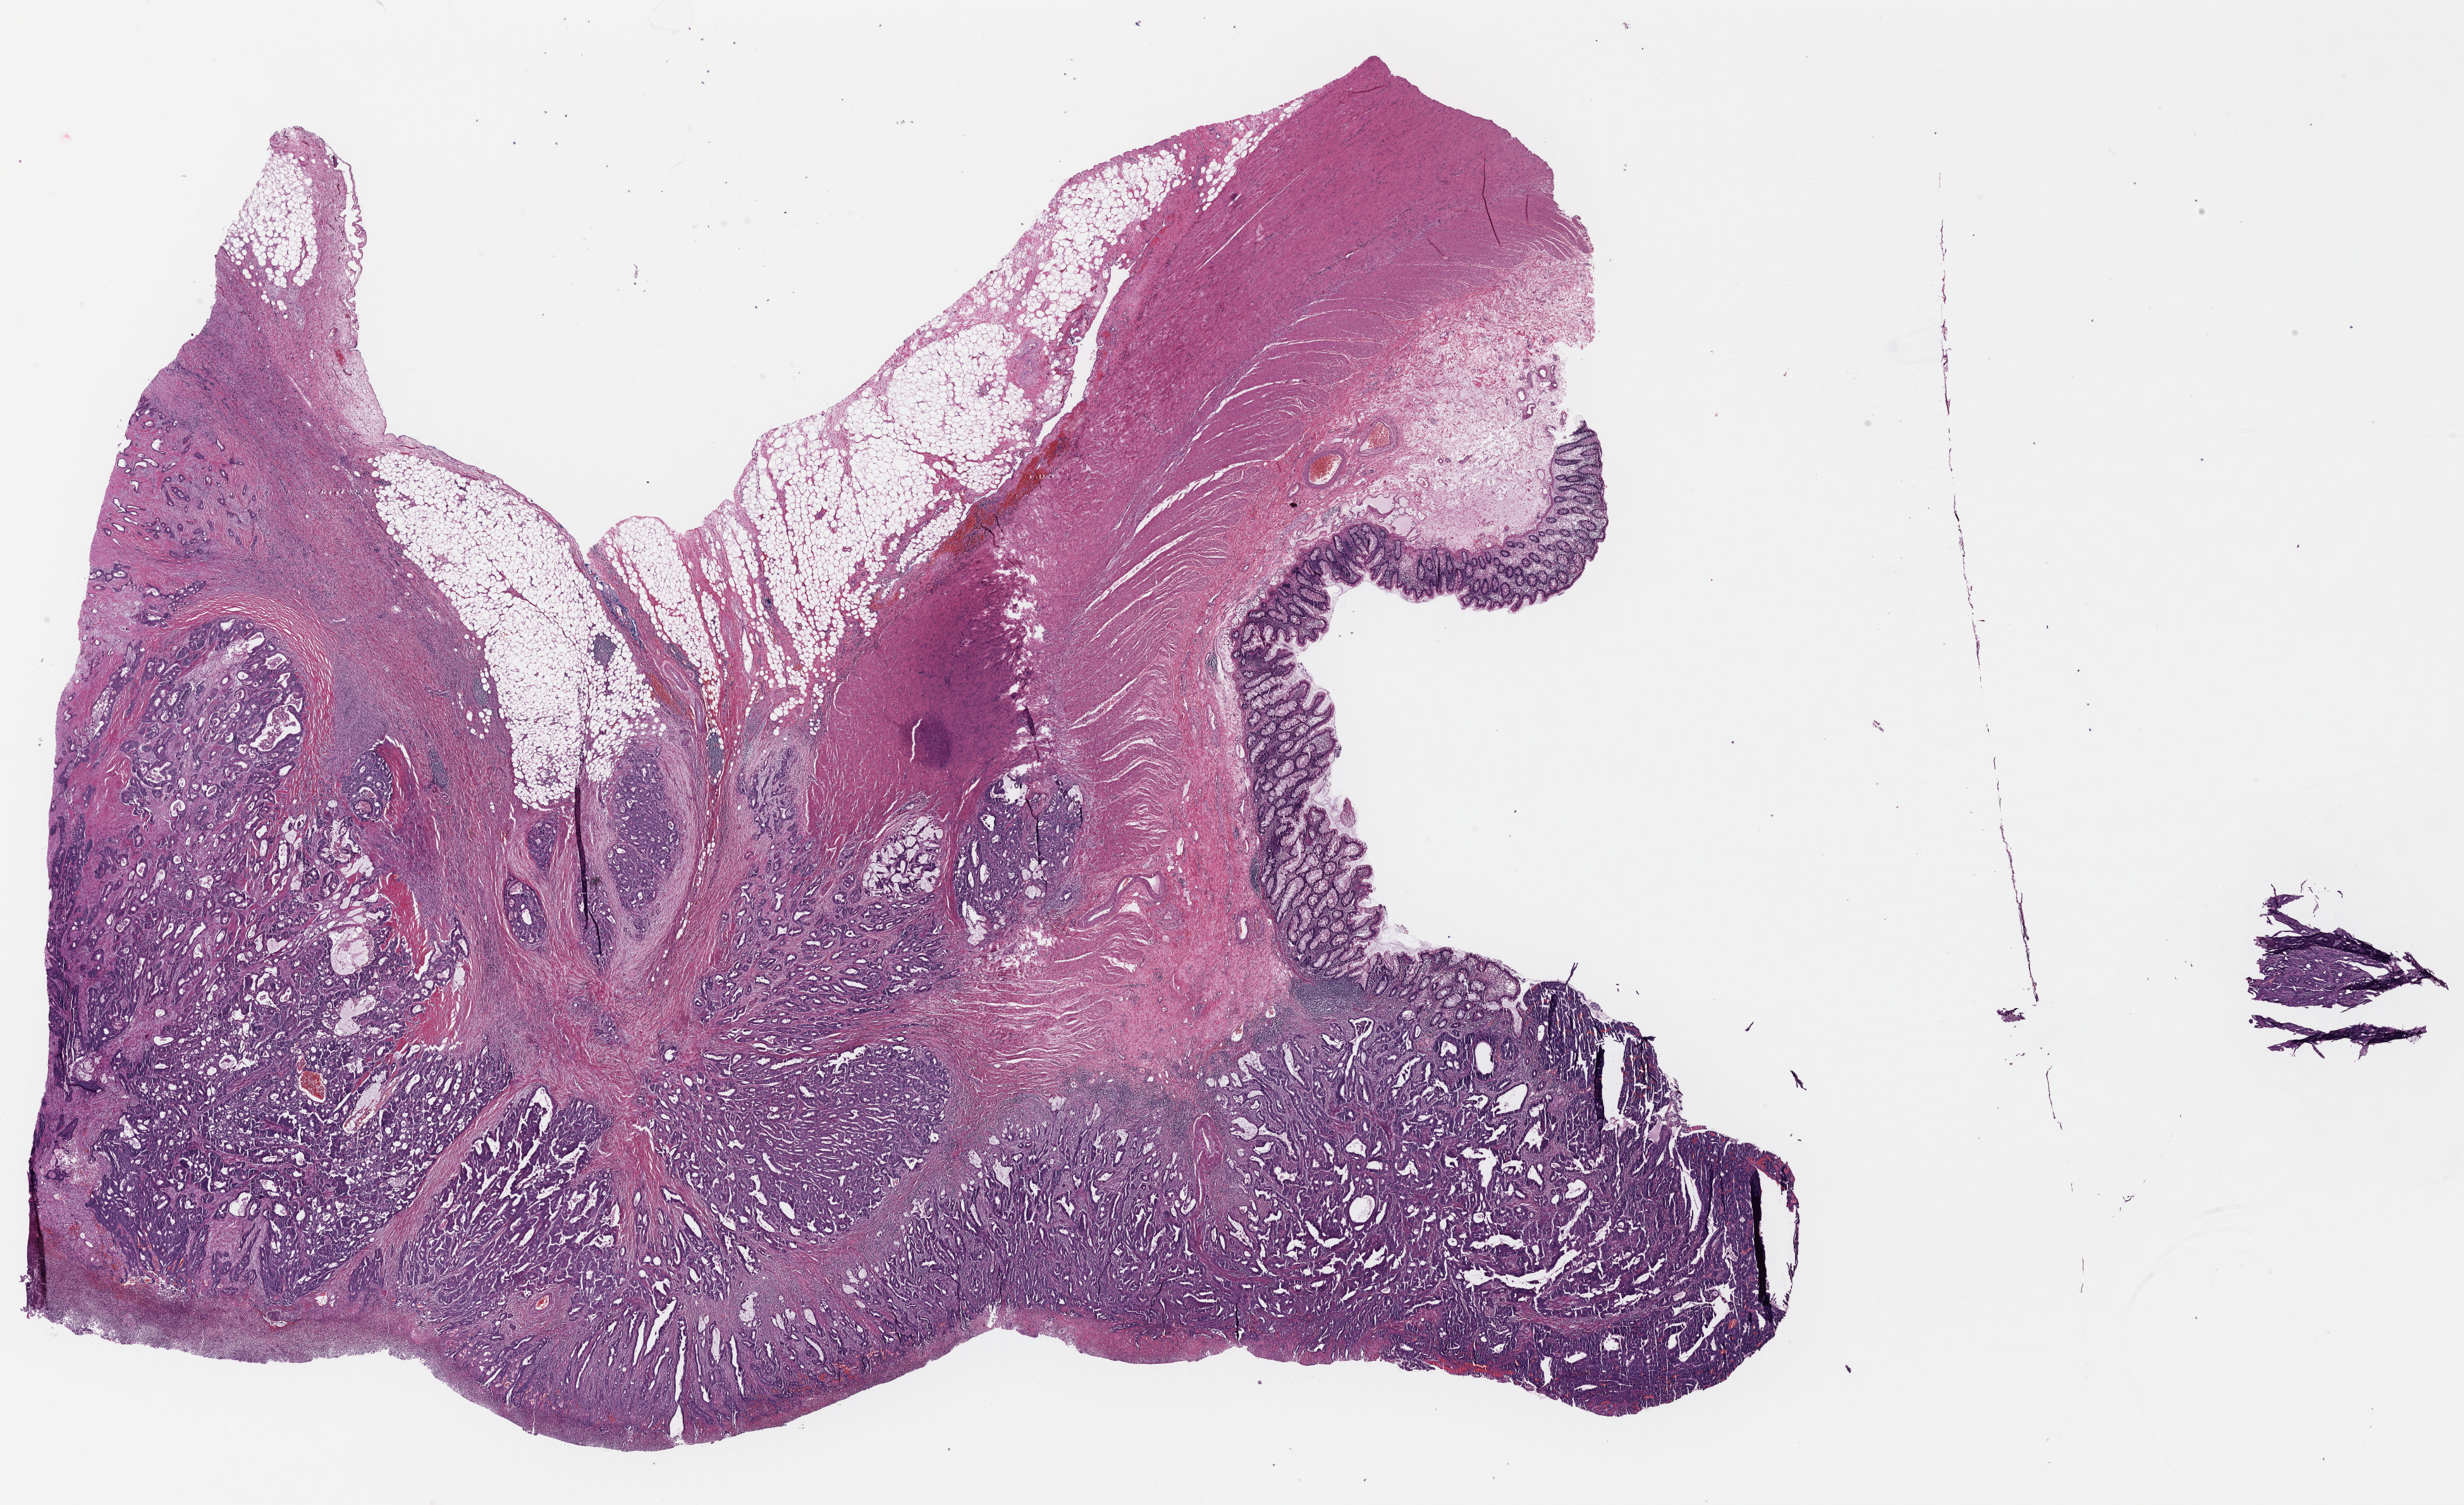
Whole-slide histology image, Hematoxylin and eosin (H&E) stained — shown as a low-resolution overview of the whole scanned area (about 30.6 x 18.7 mm, acquisition: 40x scan), formalin-fixed paraffin-embedded (FFPE) diagnostic section, primary tumour sample from the colon. Patient: male, age at initial diagnosis 69 years.
Diagnosis: Adenocarcinoma, NOS (cecum).